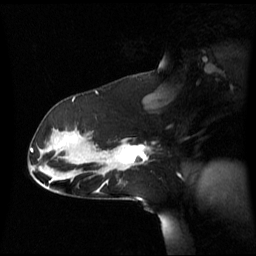
Breast MRI (dynamic contrast-enhanced), one sagittal slice. Dynamic contrast-enhanced series, image 2 of 3 at this slice position (ordered by acquisition). 1.5 T. TE 4.2 ms, TR 8.4 ms. 256 × 256 image matrix, field of view 270 × 270 mm. Female patient, age 39 years. From the clinical record (not read from this slice): setting: breast cancer imaged before/during neoadjuvant chemotherapy; receptor status: triple-negative.
Outlined on this slice (semi-automatic segmentation, software-assisted and operator-edited):
- analysis volume of interest (the breast-tissue region the enhancement analysis was run in; not a lesion): bounding box <101,139,149,173> (left, top, right, bottom; pixels)
- tumour enhancement mask (voxels above the 70 % enhancement threshold inside the analysis volume of interest): <121,145,147,163>